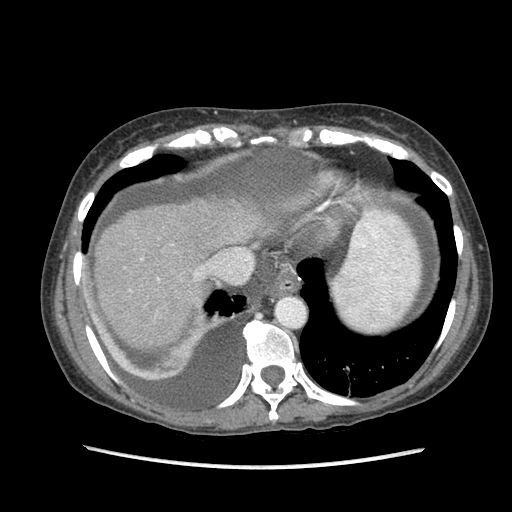
Contrast-enhanced abdominal CT (liver protocol), one axial slice. Reconstruction kernel STANDARD. Soft-tissue window (W 400 / L 40 HU). 512 × 512 image matrix. Case-level facts recorded for this patient, not image findings: diagnosis: hepatocellular carcinoma (patient treated with transarterial chemoembolisation; whether this scan precedes or follows treatment is not stated here); TNM stage (as recorded): Stage-IIIB; Child-Pugh class: A.
Annotated regions visible in this slice (semi-automatic segmentation, software-assisted and operator-edited):
- liver parenchyma outside the tumour (the mass and vessels are separate outlines, so this box may not span the whole liver): box from (x=94, y=198) to (x=270, y=348) px
- liver vessels: (x=130, y=258)–(x=201, y=291)